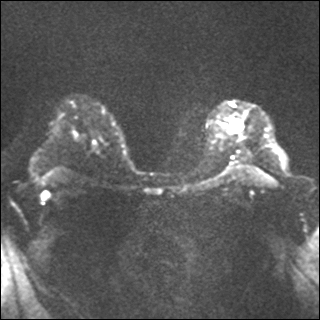
Breast MRI, one axial slice; slice 25 of 35 in the series (ordered by position); diffusion-weighted series; image 2 of 4 stored at this slice position (different b-values; order by instance number); 1.5 T; 320 × 320 image matrix, field of view 320 × 320 mm. Female patient.
Annotated regions visible in this slice (outlined manually by an expert reader):
- tumour on diffusion-weighted imaging: box from (x=232, y=120) to (x=241, y=131) px